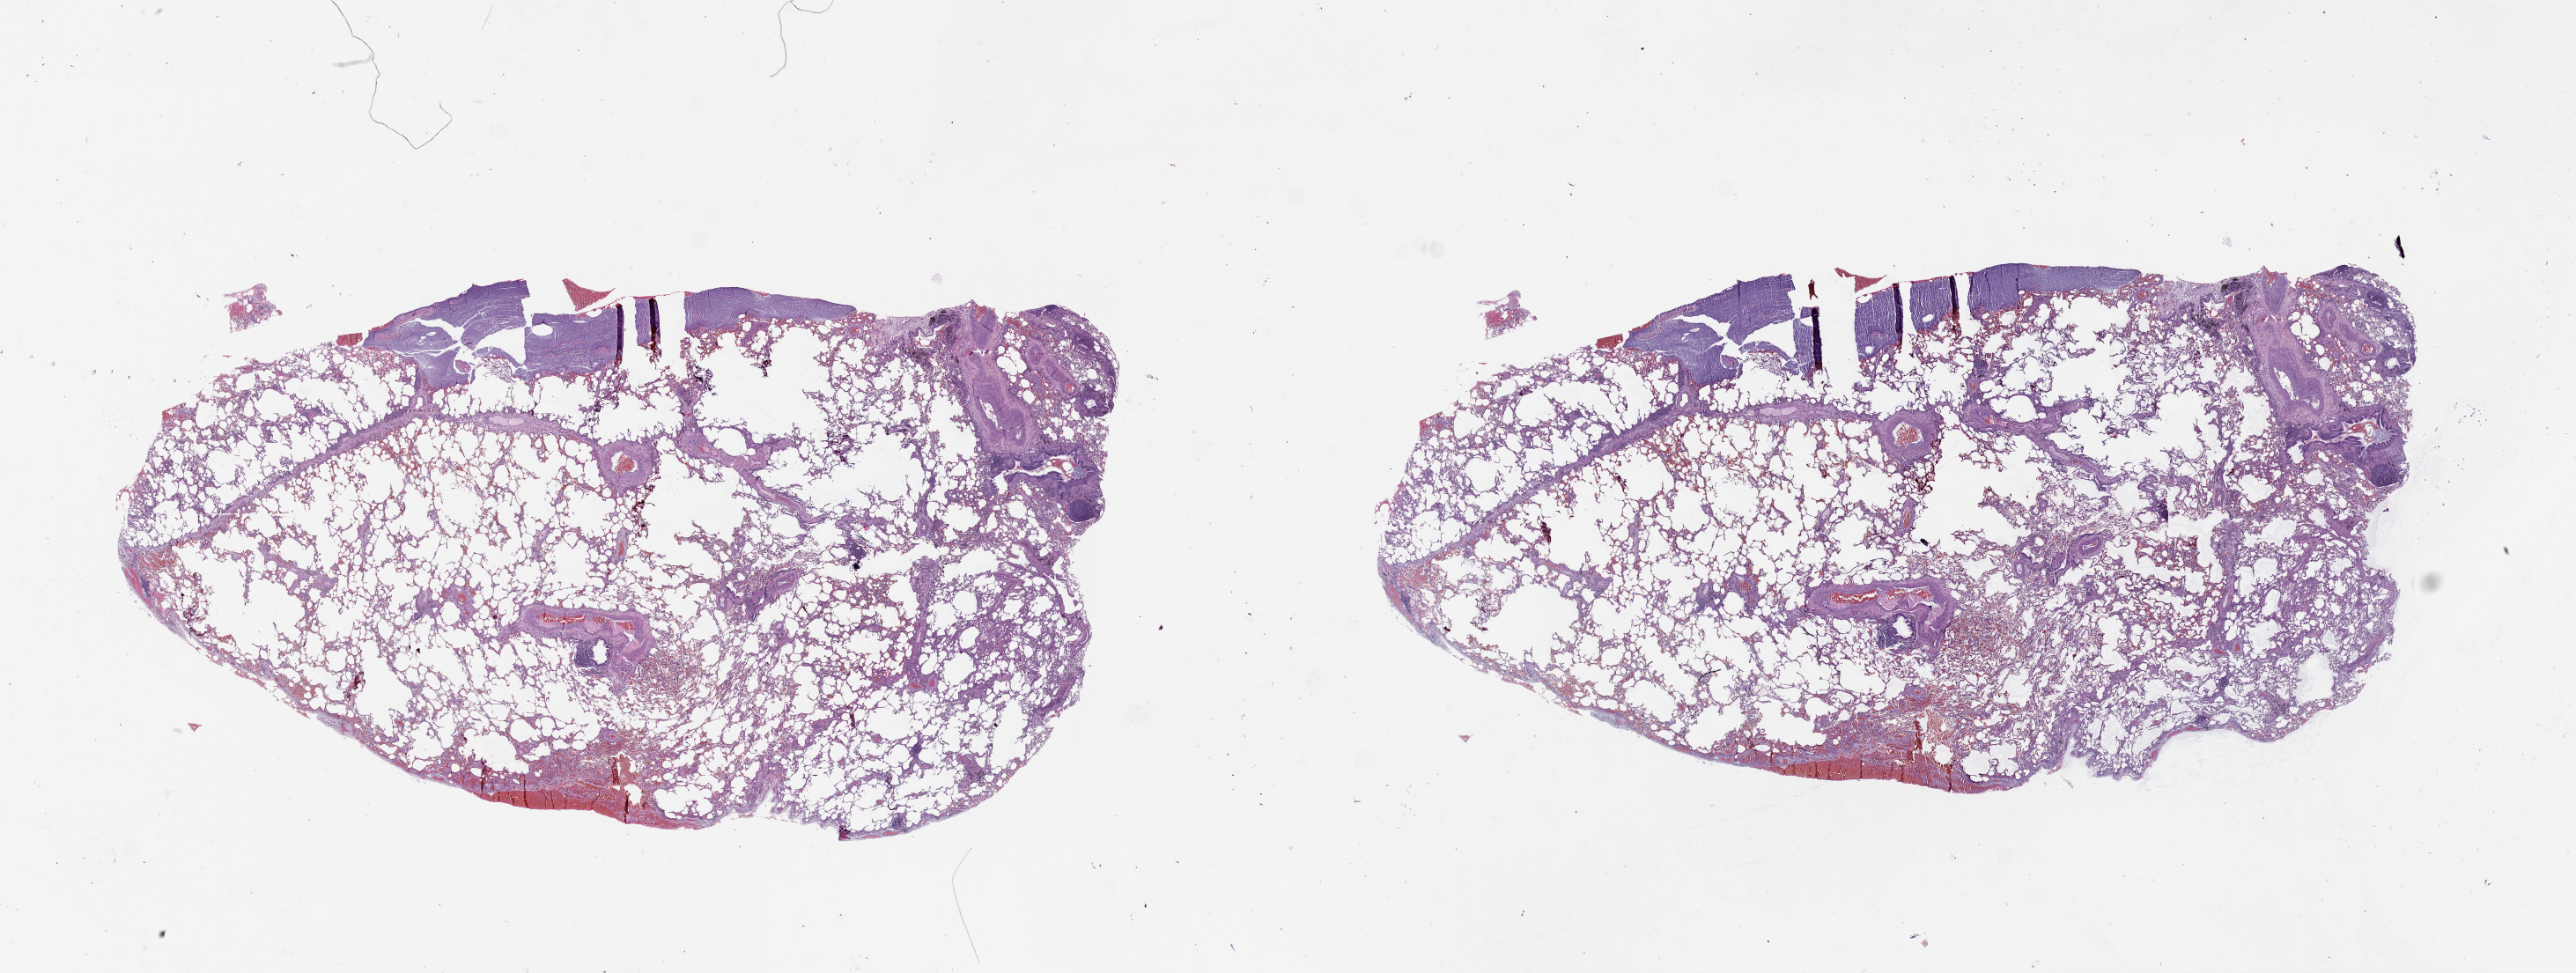
Digitized H&E tissue section (whole slide) — a low-resolution overview of the entire scanned area, about 47.1 x 17.8 mm (slide scanned at 20x). Lung, tissue type not recorded.
Patient diagnosis (cohort enrolment): squamous cell carcinoma (lung).